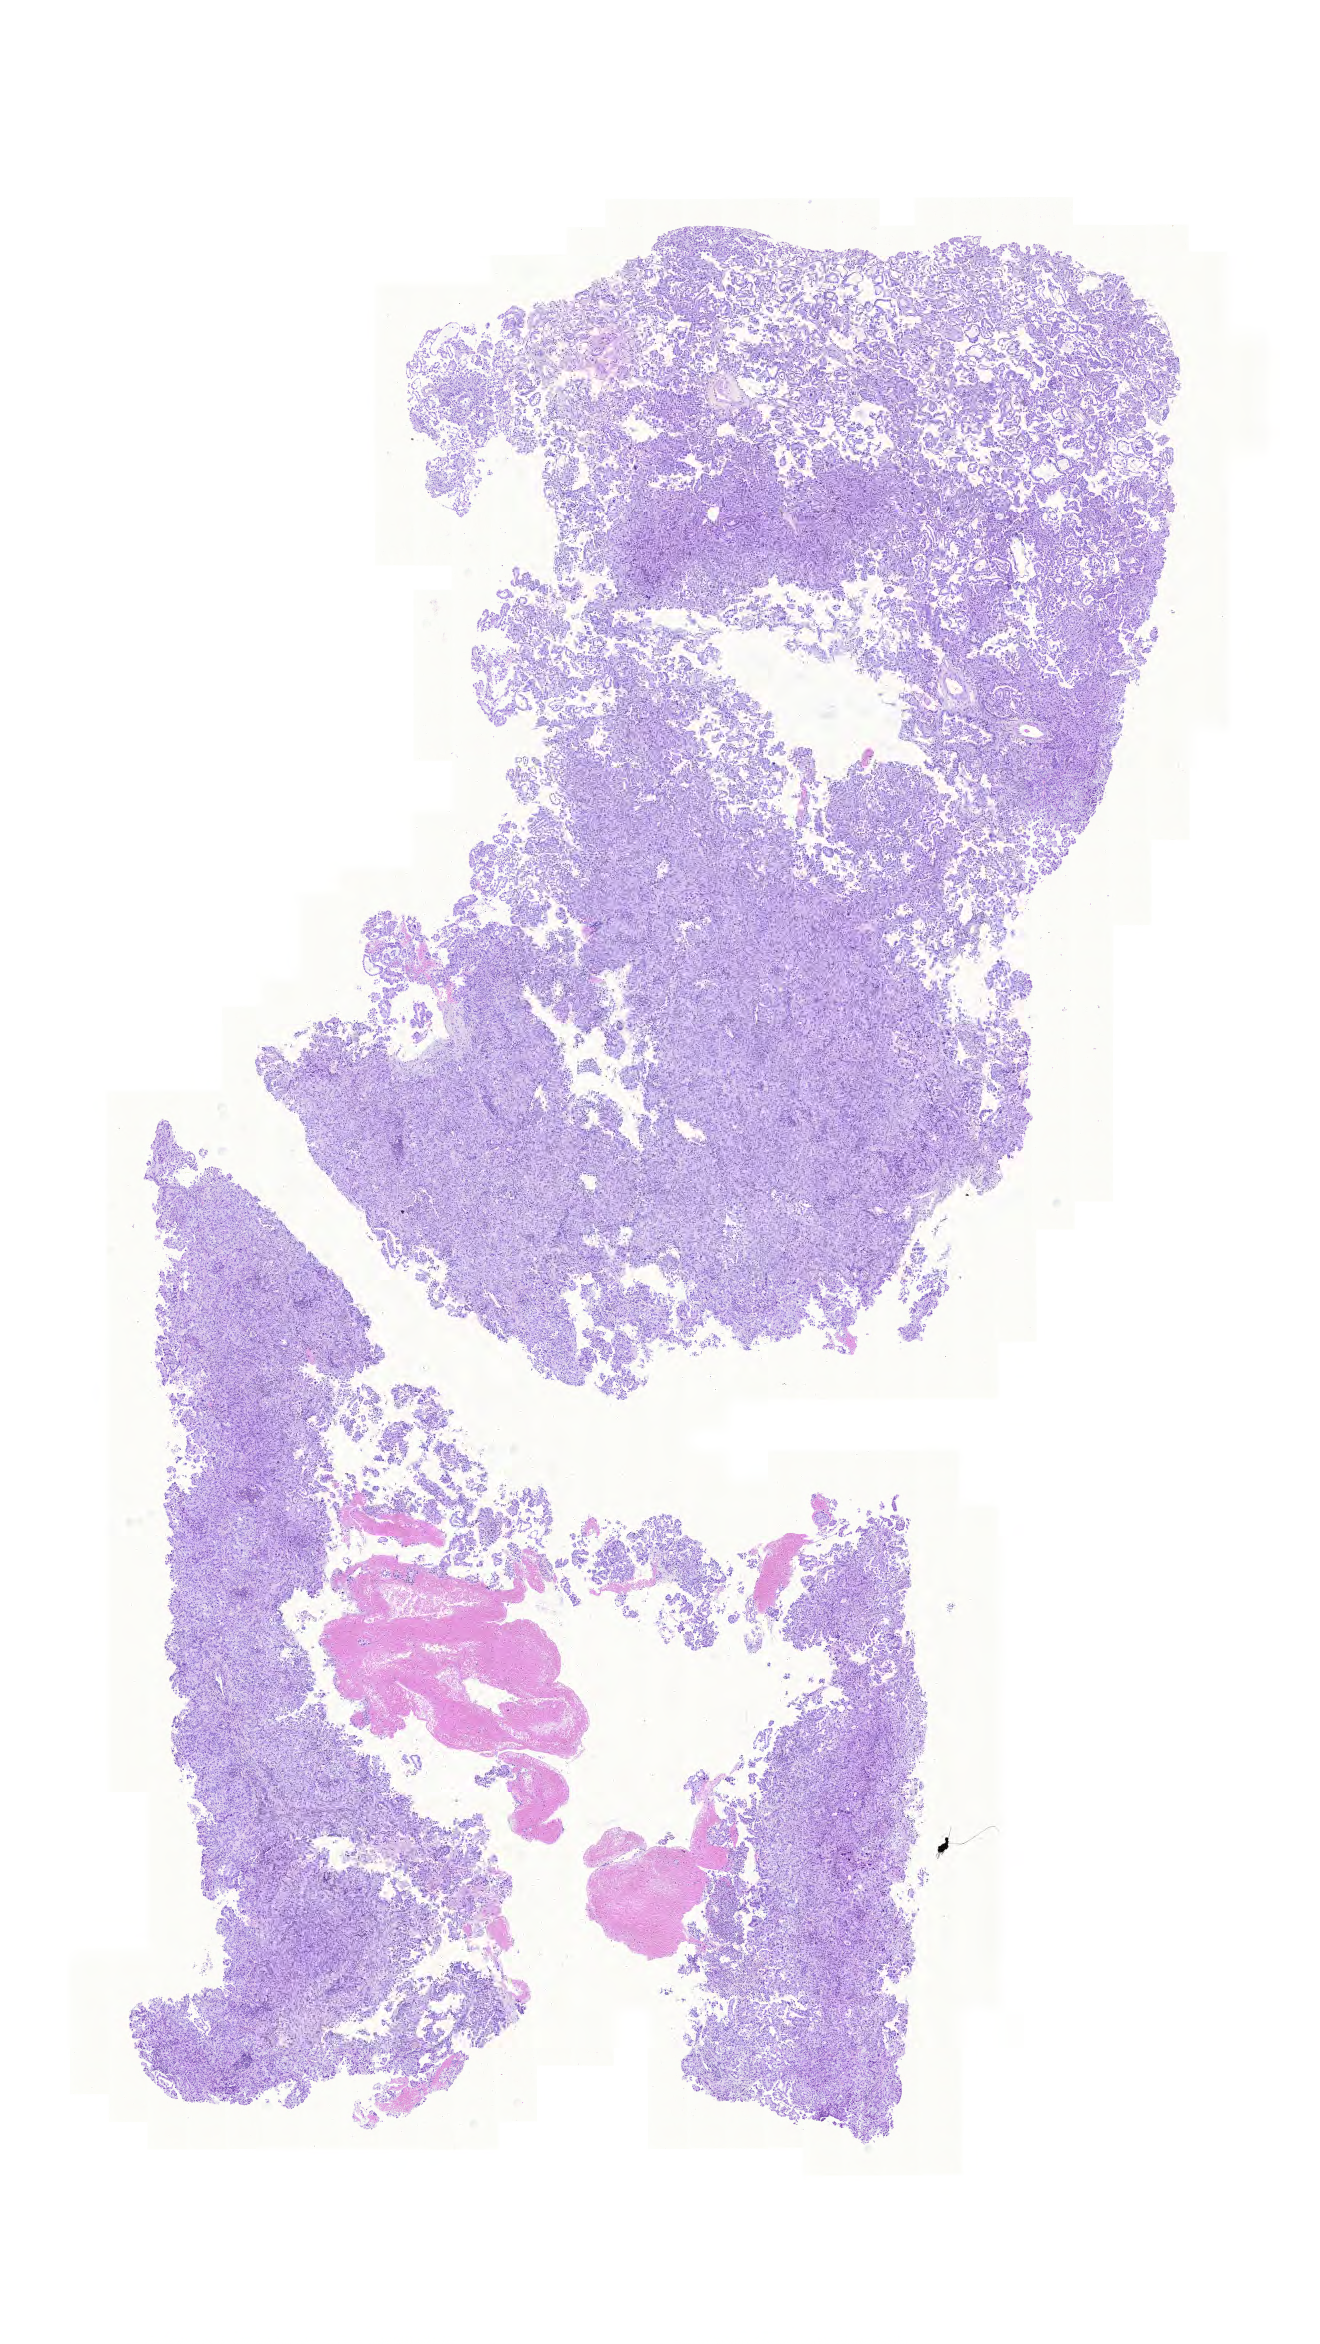
Whole-slide histology image, H&E, a low-resolution overview of the entire scanned area, about 9.8 x 17.4 mm; formalin-fixed paraffin-embedded (FFPE) diagnostic section; sample: primary tumour, lung. Male, age 71 years at initial diagnosis.
Histologic diagnosis: Adenocarcinoma with mixed subtypes (lower lobe, lung). TNM: T2 N0 M0. AJCC pathologic stage: IB. Laterality: left.